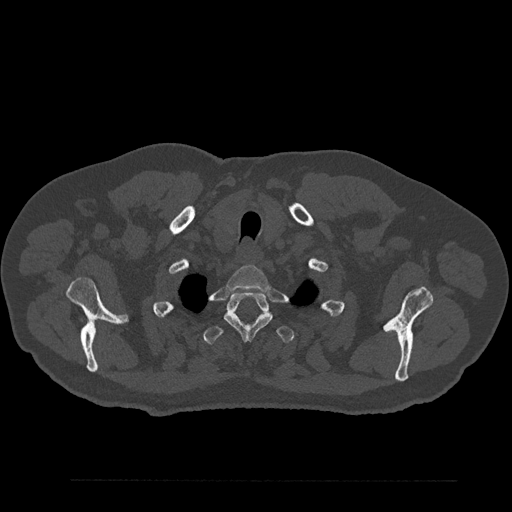
CT including the spine, one axial slice; 120 kVp; bone window (W 1800 / L 400 HU); 0.5 mm slice thickness; 512 × 512 image matrix. Patient: male, 61 years. From the clinical record (not read from this slice): primary cancer: prostate.
Outlined on this slice (semi-automatic segmentation, software-assisted and operator-edited):
- T1 vertebra: bounding box <227,265,270,291> (left, top, right, bottom; pixels)
- T2 vertebra: <224,292,272,341>
- T3 vertebra: <203,326,295,345>